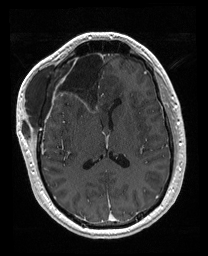
Brain MRI from a brain-tumour surgery series, one axial slice. Position 85 of 176 along the scan axis. T1-weighted post-contrast. 1 mm slice thickness. 208 × 256 image matrix, field of view 208 × 256 mm. From the clinical record (not read from this slice): histopathology: Astrocytoma; WHO grade: 4.
Outlined on this slice (expert manual segmentation):
- previous resection cavity: bounding box [x1, y1, x2, y2] px = [56, 52, 106, 111]